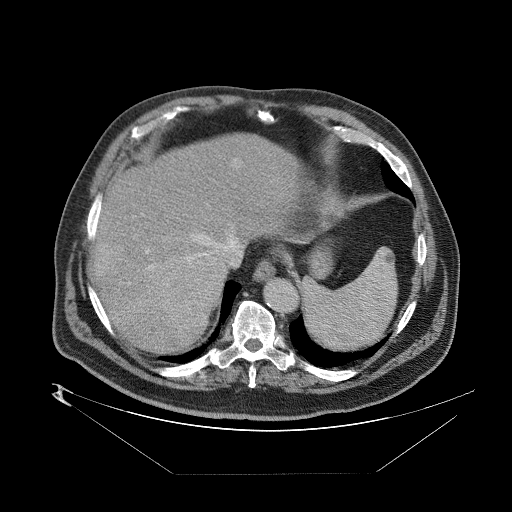
Contrast-enhanced abdominal CT (liver protocol), one axial slice; position 67 of 89 along the scan axis; reconstruction kernel STANDARD; 140 kVp; one of 2 acquisitions stored at this slice position; soft-tissue window (W 400 / L 40 HU); 2.5 mm slice thickness; 512 × 512 image matrix, field of view 480 × 480 mm. Case-level facts recorded for this patient, not image findings: diagnosis: hepatocellular carcinoma (patient treated with transarterial chemoembolisation; whether this scan precedes or follows treatment is not stated here); TNM stage (as recorded): Stage-II.
Outlined on this slice (semi-automatic segmentation, software-assisted and operator-edited):
- abdominal aorta: box from (x=264, y=281) to (x=298, y=314) px
- liver parenchyma outside the tumour (the mass and vessels are separate outlines, so this box may not span the whole liver): (x=88, y=130)–(x=304, y=350)
- mass: (x=155, y=249)–(x=225, y=320)
- liver vessels: (x=101, y=157)–(x=240, y=327)